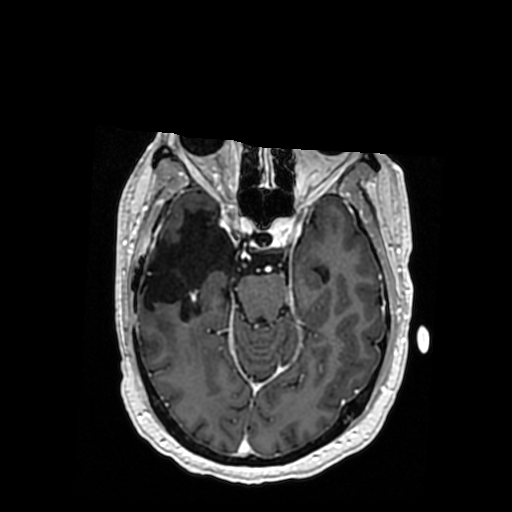
Brain MRI from a brain-tumour surgery series, one axial slice; position 222 of 364 along the scan axis; T1-weighted post-contrast; 512 × 512 image matrix, field of view 260 × 260 mm. From the clinical record (not read from this slice): histopathology: Oligodendroglioma; WHO grade: 3; IDH mutation: yes.
Annotated regions visible in this slice (outlined manually by an expert reader):
- previous resection cavity: bounding box (x1, y1, x2, y2) in pixels: (141, 208, 235, 319)